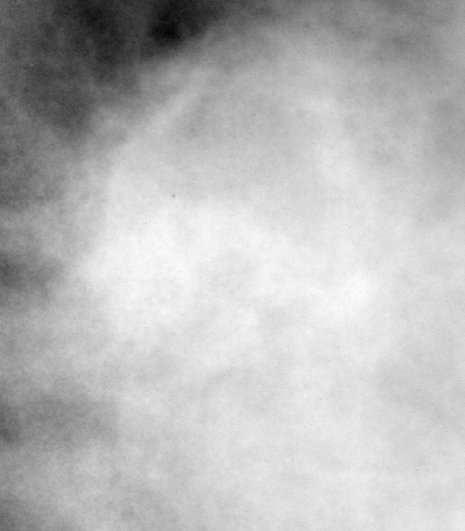
Crop from a digitized film mammogram around one marked abnormality, left breast, MLO view.
Mass, shape focal asymmetric density; BI-RADS assessment category 3; subtlety rating 1 on a 1 (subtle) to 5 (obvious) scale; pathology result (as recorded, not read from the image): malignant.